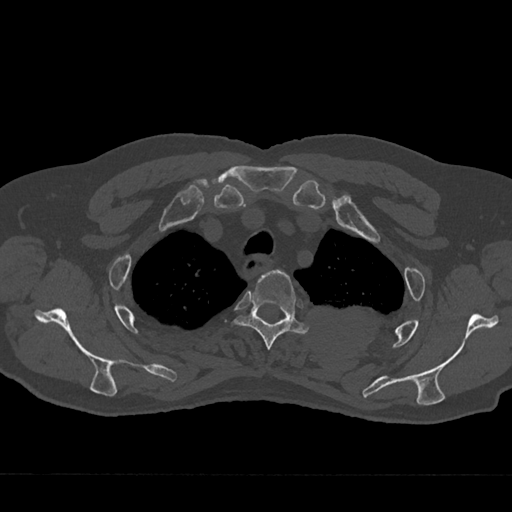
CT including the spine, one axial slice; slice 570 of 797 in the series (ordered by position); reconstruction kernel Br40s/3; 120 kVp; bone window (W 1800 / L 400 HU); 512 × 512 image matrix. Male patient, age 75 years. From the clinical record (not read from this slice): primary cancer: renal; vertebrae with lytic lesions (as recorded): T4.
Structures marked on this image (semi-automatic segmentation, software-assisted and operator-edited):
- T3 vertebra: bounding box <235,270,309,350> (left, top, right, bottom; pixels)